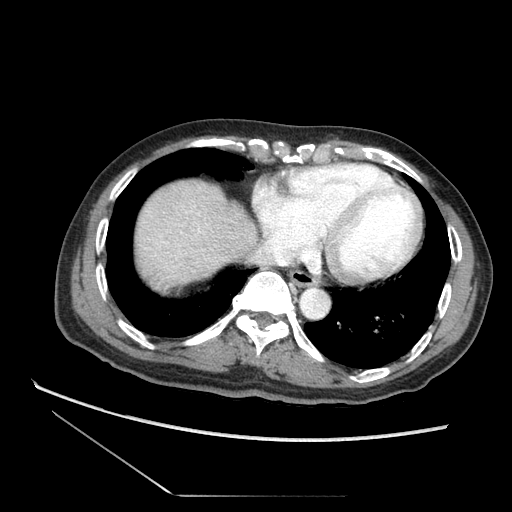
Contrast-enhanced abdominal CT (liver protocol), one axial slice; position 70 of 73 along the scan axis; 120 kVp; soft-tissue window (W 400 / L 40 HU); 2.5 mm slice thickness; 512 × 512 image matrix. Case-level facts recorded for this patient, not image findings: diagnosis: hepatocellular carcinoma (patient treated with transarterial chemoembolisation; whether this scan precedes or follows treatment is not stated here); TNM stage (as recorded): Stage-II; Child-Pugh class: A.
Structures marked on this image (semi-automatic segmentation, software-assisted and operator-edited):
- abdominal aorta: bounding box (x1, y1, x2, y2) in pixels: (302, 289, 330, 318)
- liver parenchyma outside the tumour (the mass and vessels are separate outlines, so this box may not span the whole liver): (126, 176, 263, 298)